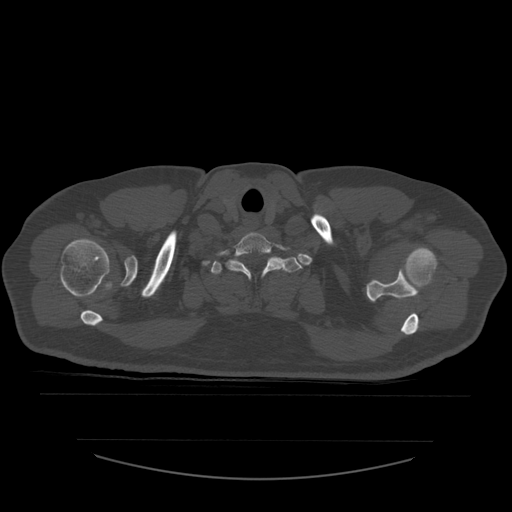
CT including the spine, one axial slice; slice 477 of 532 in the series (ordered by position); bone window (W 1800 / L 400 HU); 512 × 512 image matrix. Patient age 44 years. Case-level facts recorded for this patient, not image findings: primary cancer: soft tissue sarcoma.
Annotated regions visible in this slice (semi-automatic segmentation, software-assisted and operator-edited):
- T1 vertebra: box from (x=211, y=257) to (x=303, y=275) px